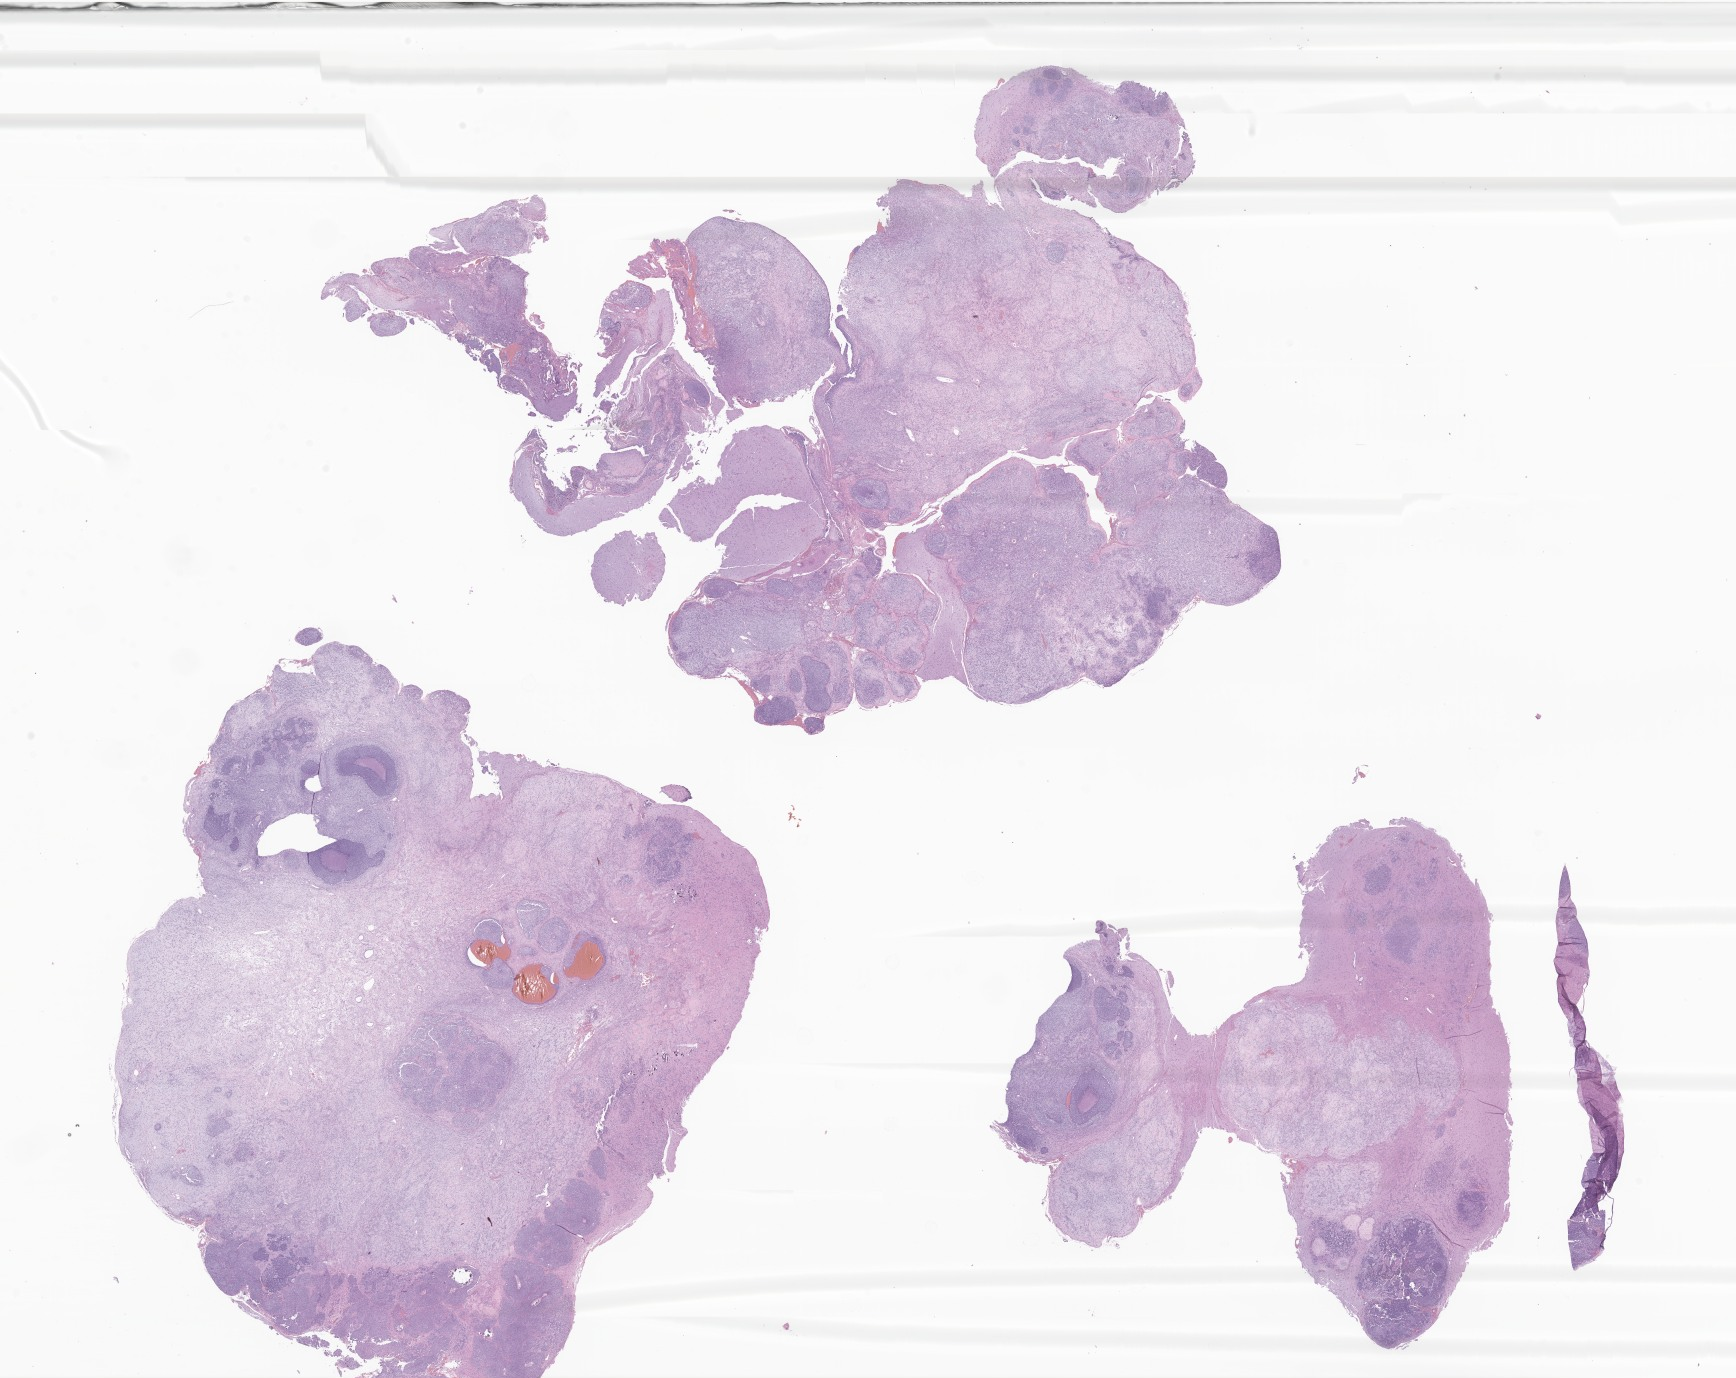
Hematoxylin and eosin (H&E) whole-slide image of tumor tissue from the temporal lobe, a low-resolution overview of the entire scanned area, about 29.3 x 23.2 mm; formalin-fixed paraffin-embedded section. Male patient, age 42 months (3 years 6 months).
• diagnosis (ICD-O-3 morphology term): Neoplasm, malignant